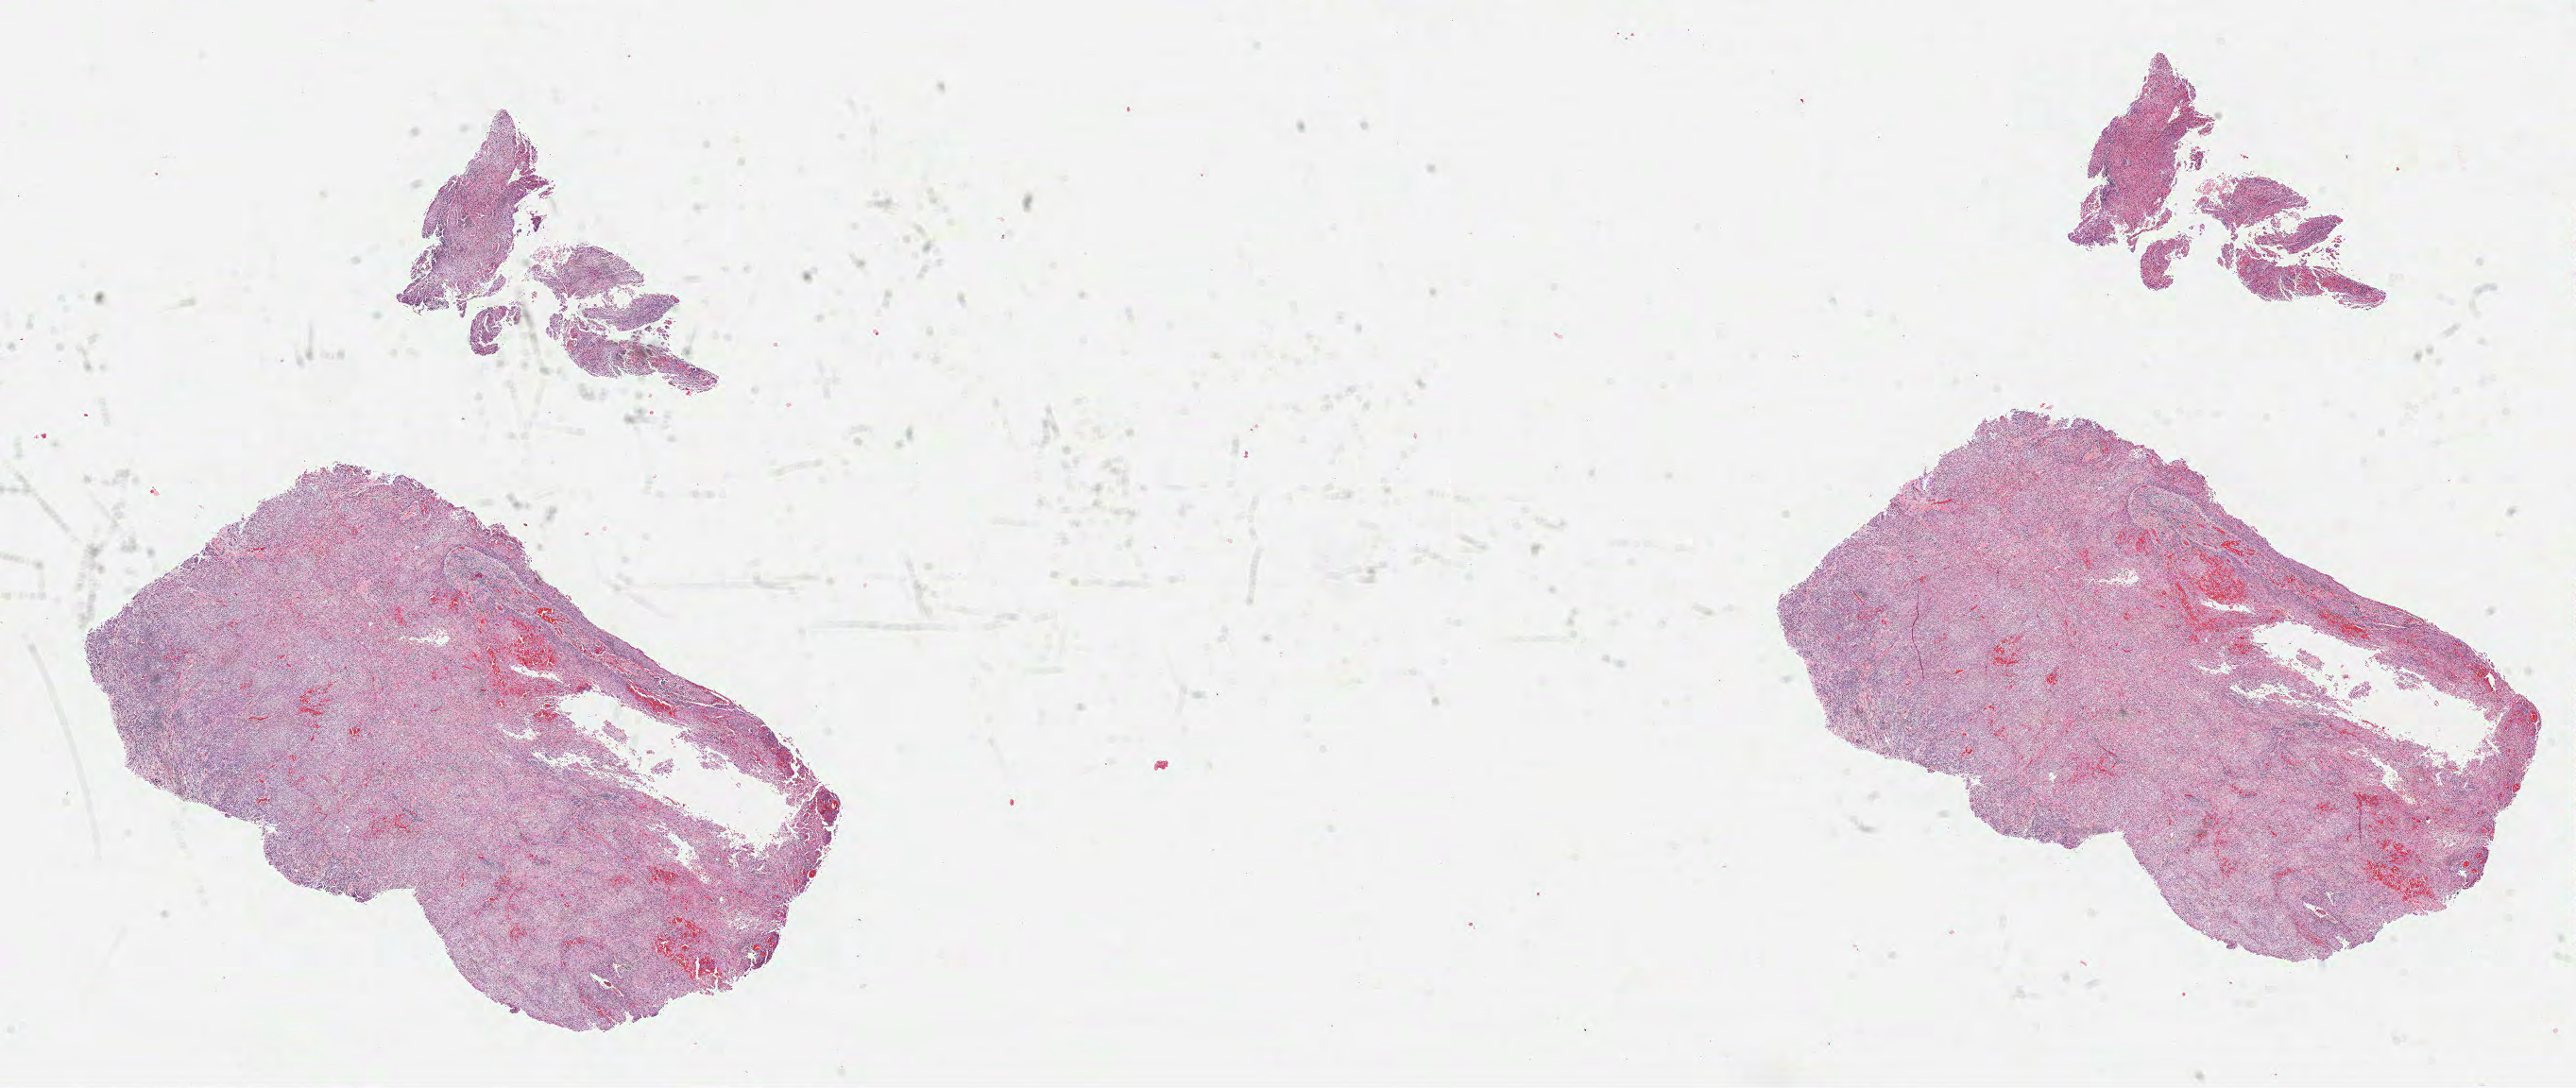
H&E whole-slide image — a low-resolution overview of the entire scanned area, about 22.0 x 9.3 mm (from a 40x scan); formalin-fixed paraffin-embedded (FFPE) diagnostic section; head and neck, primary tumour sample. Male patient; age at initial diagnosis 56 years. Histologic grade: G3 (poorly differentiated).
AJCC pathologic stage: IVA. Pathologic diagnosis: Squamous cell carcinoma, NOS (gum, NOS).